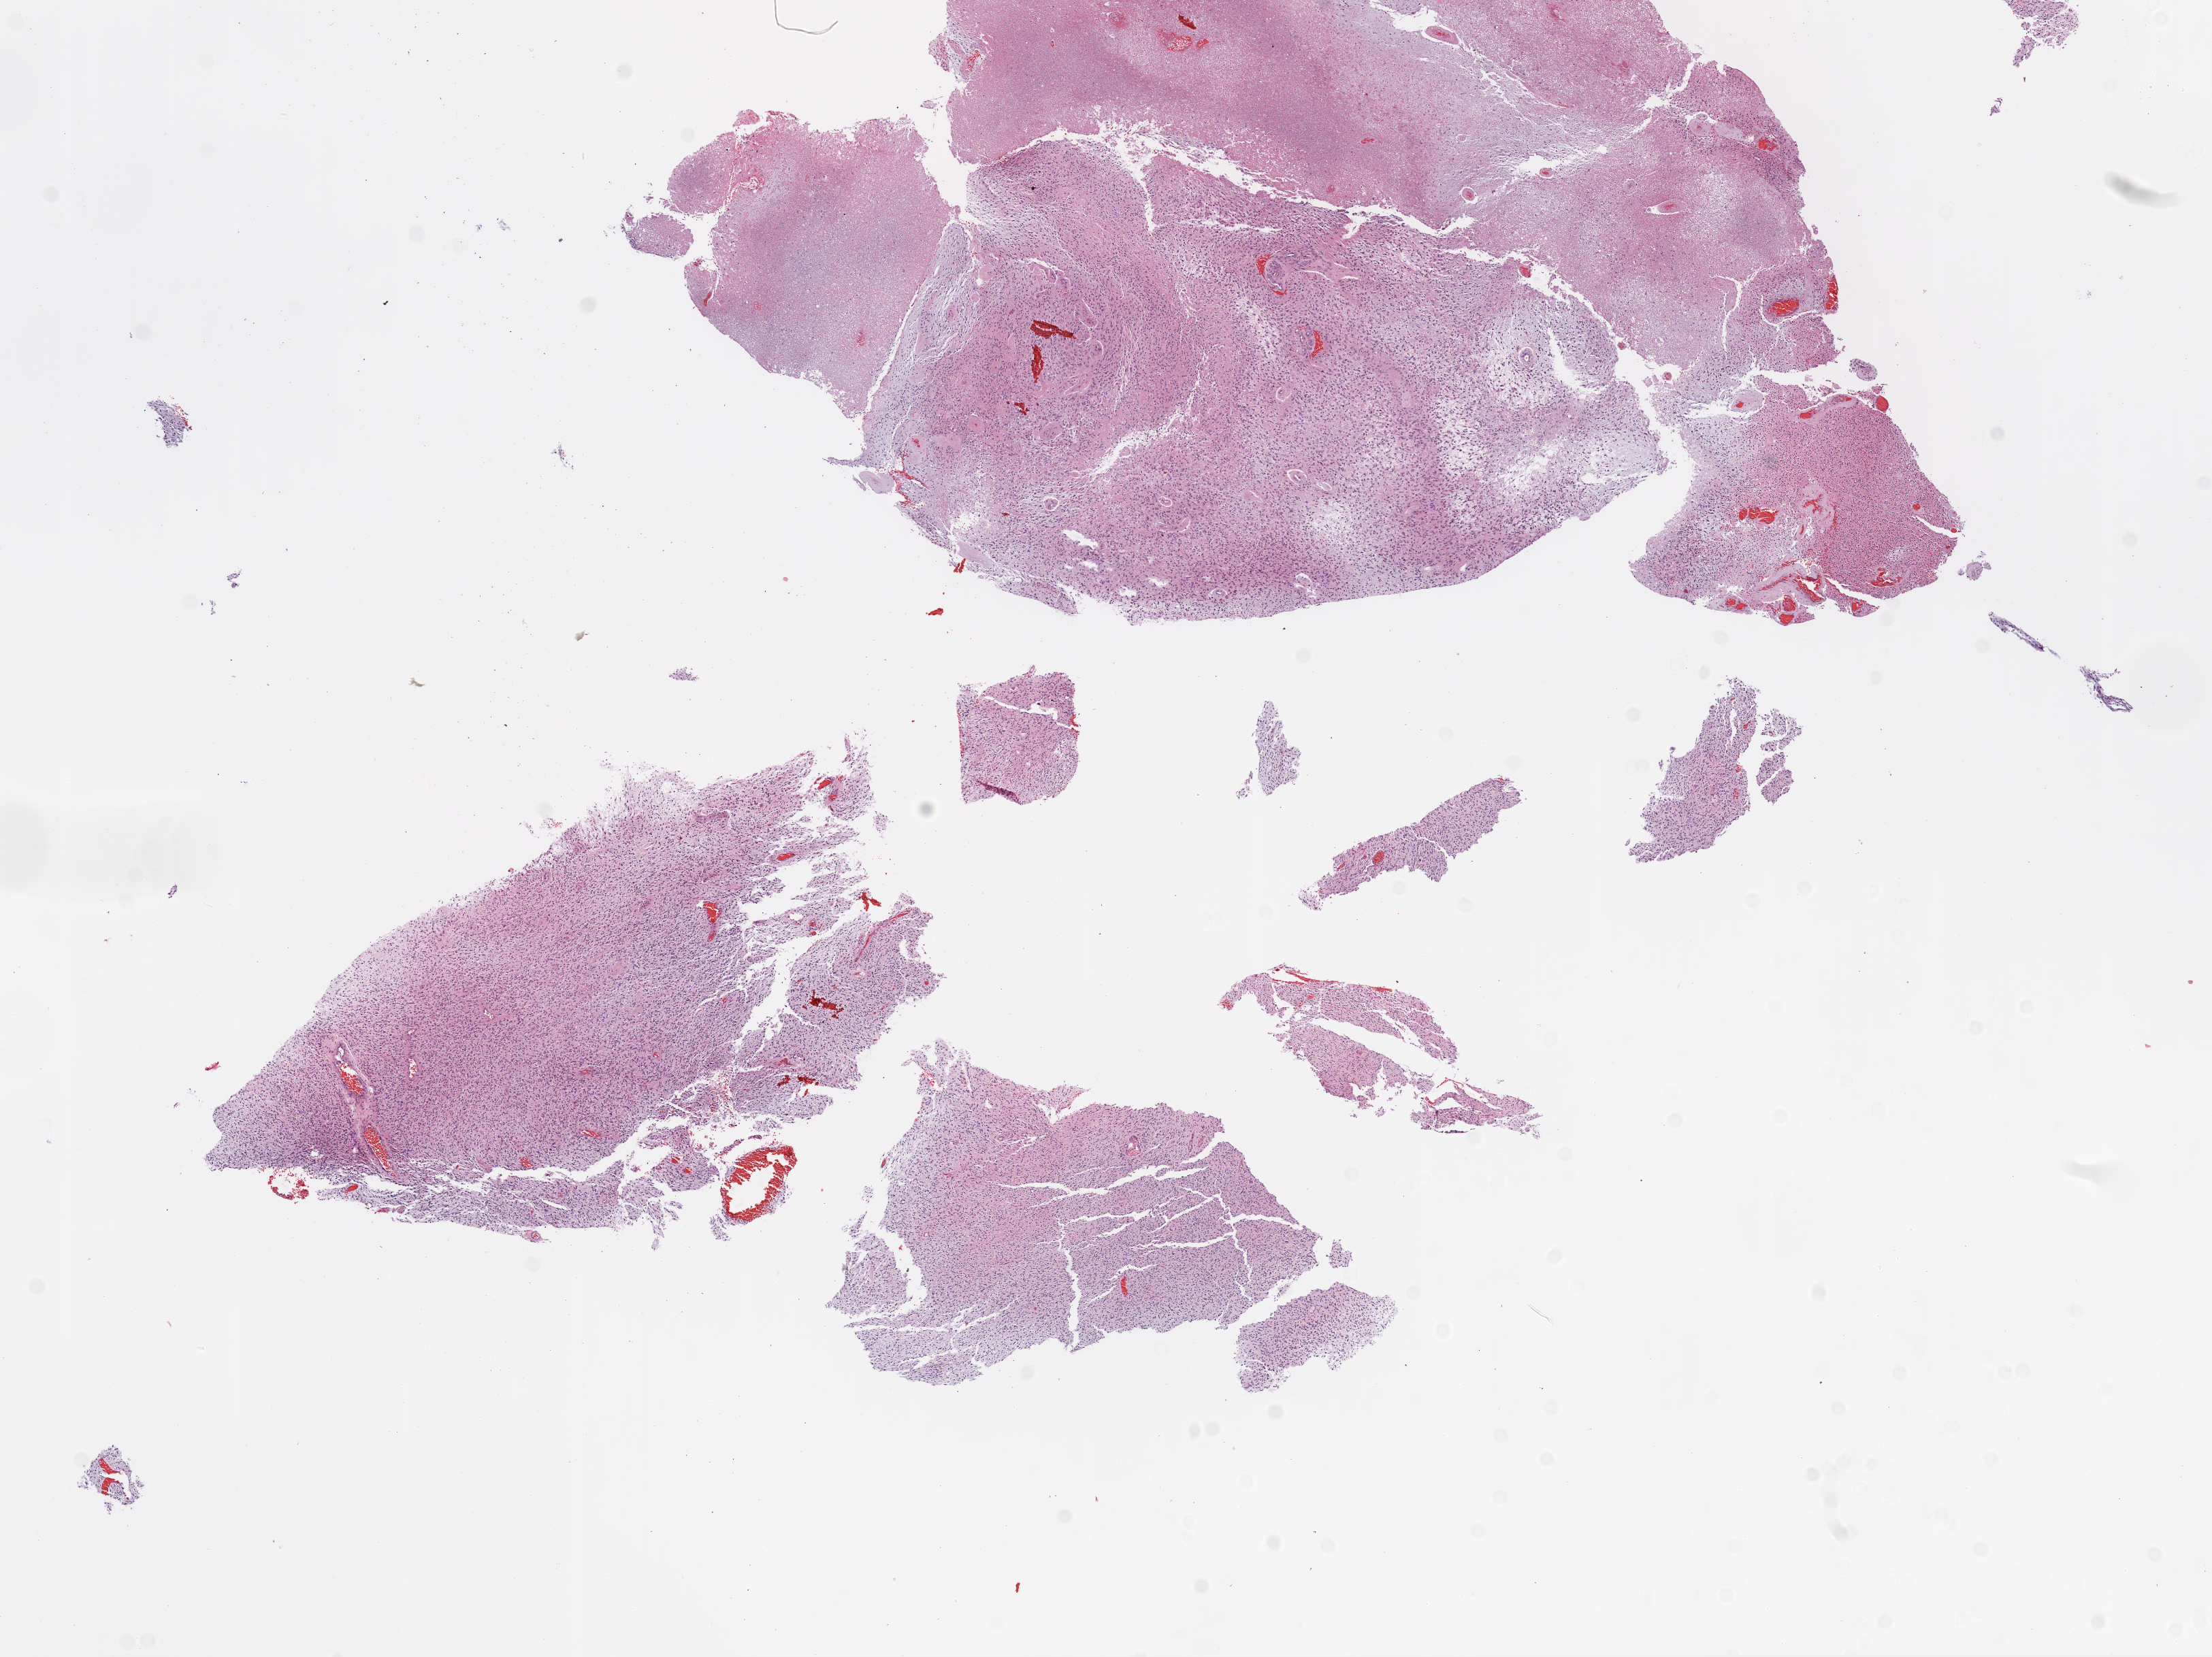
H&E whole-slide image, a low-resolution overview of the entire scanned area, about 13.0 x 9.8 mm (from a 20x scan); formalin-fixed paraffin-embedded (FFPE) diagnostic section; brain, primary tumour sample. Female, age 84 years at initial diagnosis.
Pathologic diagnosis: Glioblastoma.